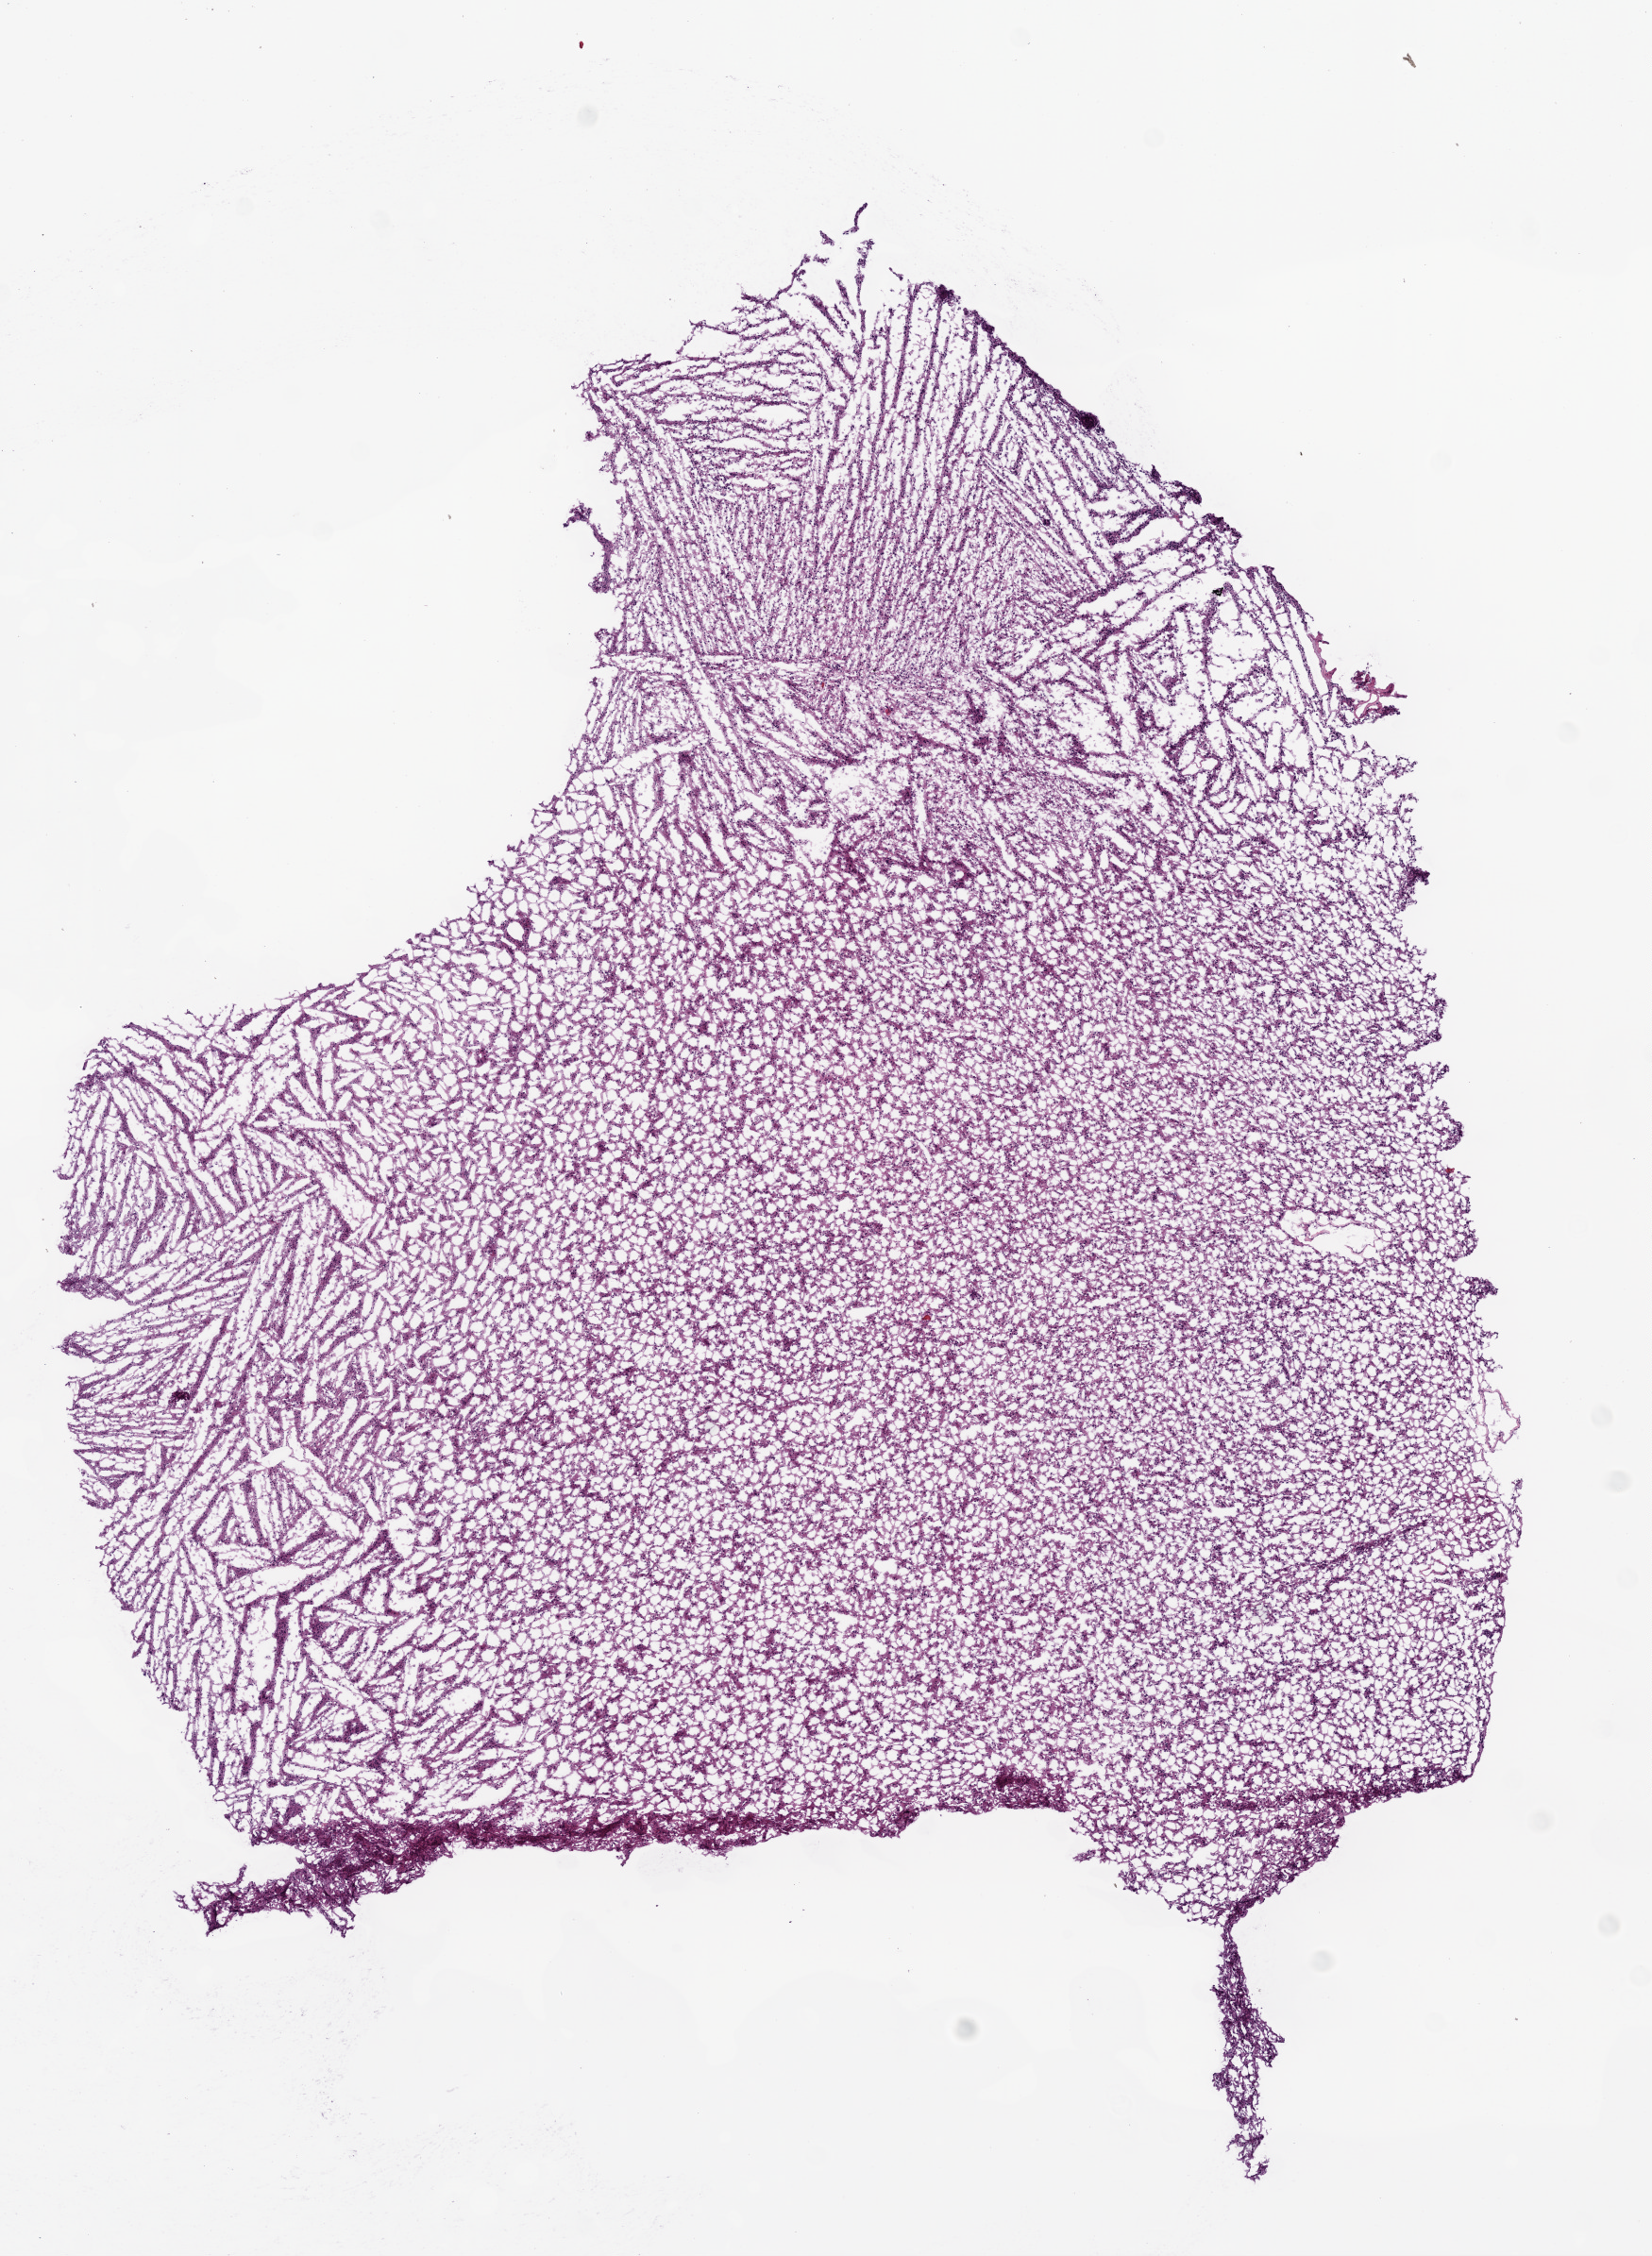
Whole-slide histology image, H&E-stained, whole scanned area (about 7.0 x 9.6 mm, acquisition: 20x scan) shown as a low-resolution overview; frozen section from the bottom of the tissue portion; brain, primary tumour sample. Patient: female, age at initial diagnosis 69 years. Slide review estimates, as recorded: tumour cells 90%, tumour nuclei 90%, normal cells 0%, stromal cells 10%, necrosis 0%.
Diagnosis: Glioblastoma.